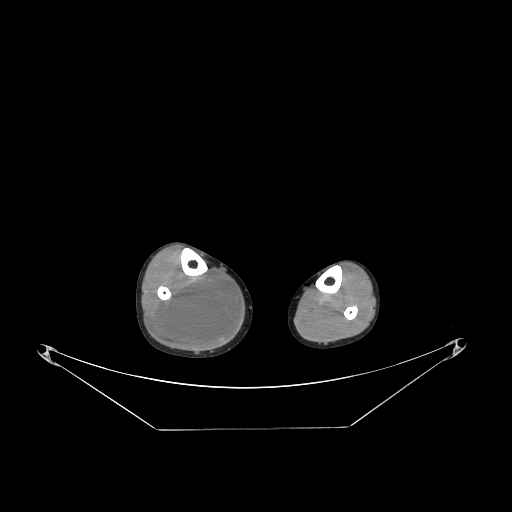
CT of an extremity soft-tissue mass (from a PET/CT study), one axial slice. Slice 93 of 267 in the series (ordered by position). 140 kVp. Soft-tissue window (W 400 / L 40 HU). 3.75 mm slice thickness. 512 × 512 image matrix. Male patient. From the clinical record (not read from this slice): histological type: liposarcoma - round cell; grade: high; site of the primary tumour: right calf.
Outlined on this slice (expert contour drawn on MRI and transferred to this co-registered scan by the dataset authors):
- gross tumour volume (mass): bounding box (x1, y1, x2, y2) in pixels: (153, 272, 239, 350)